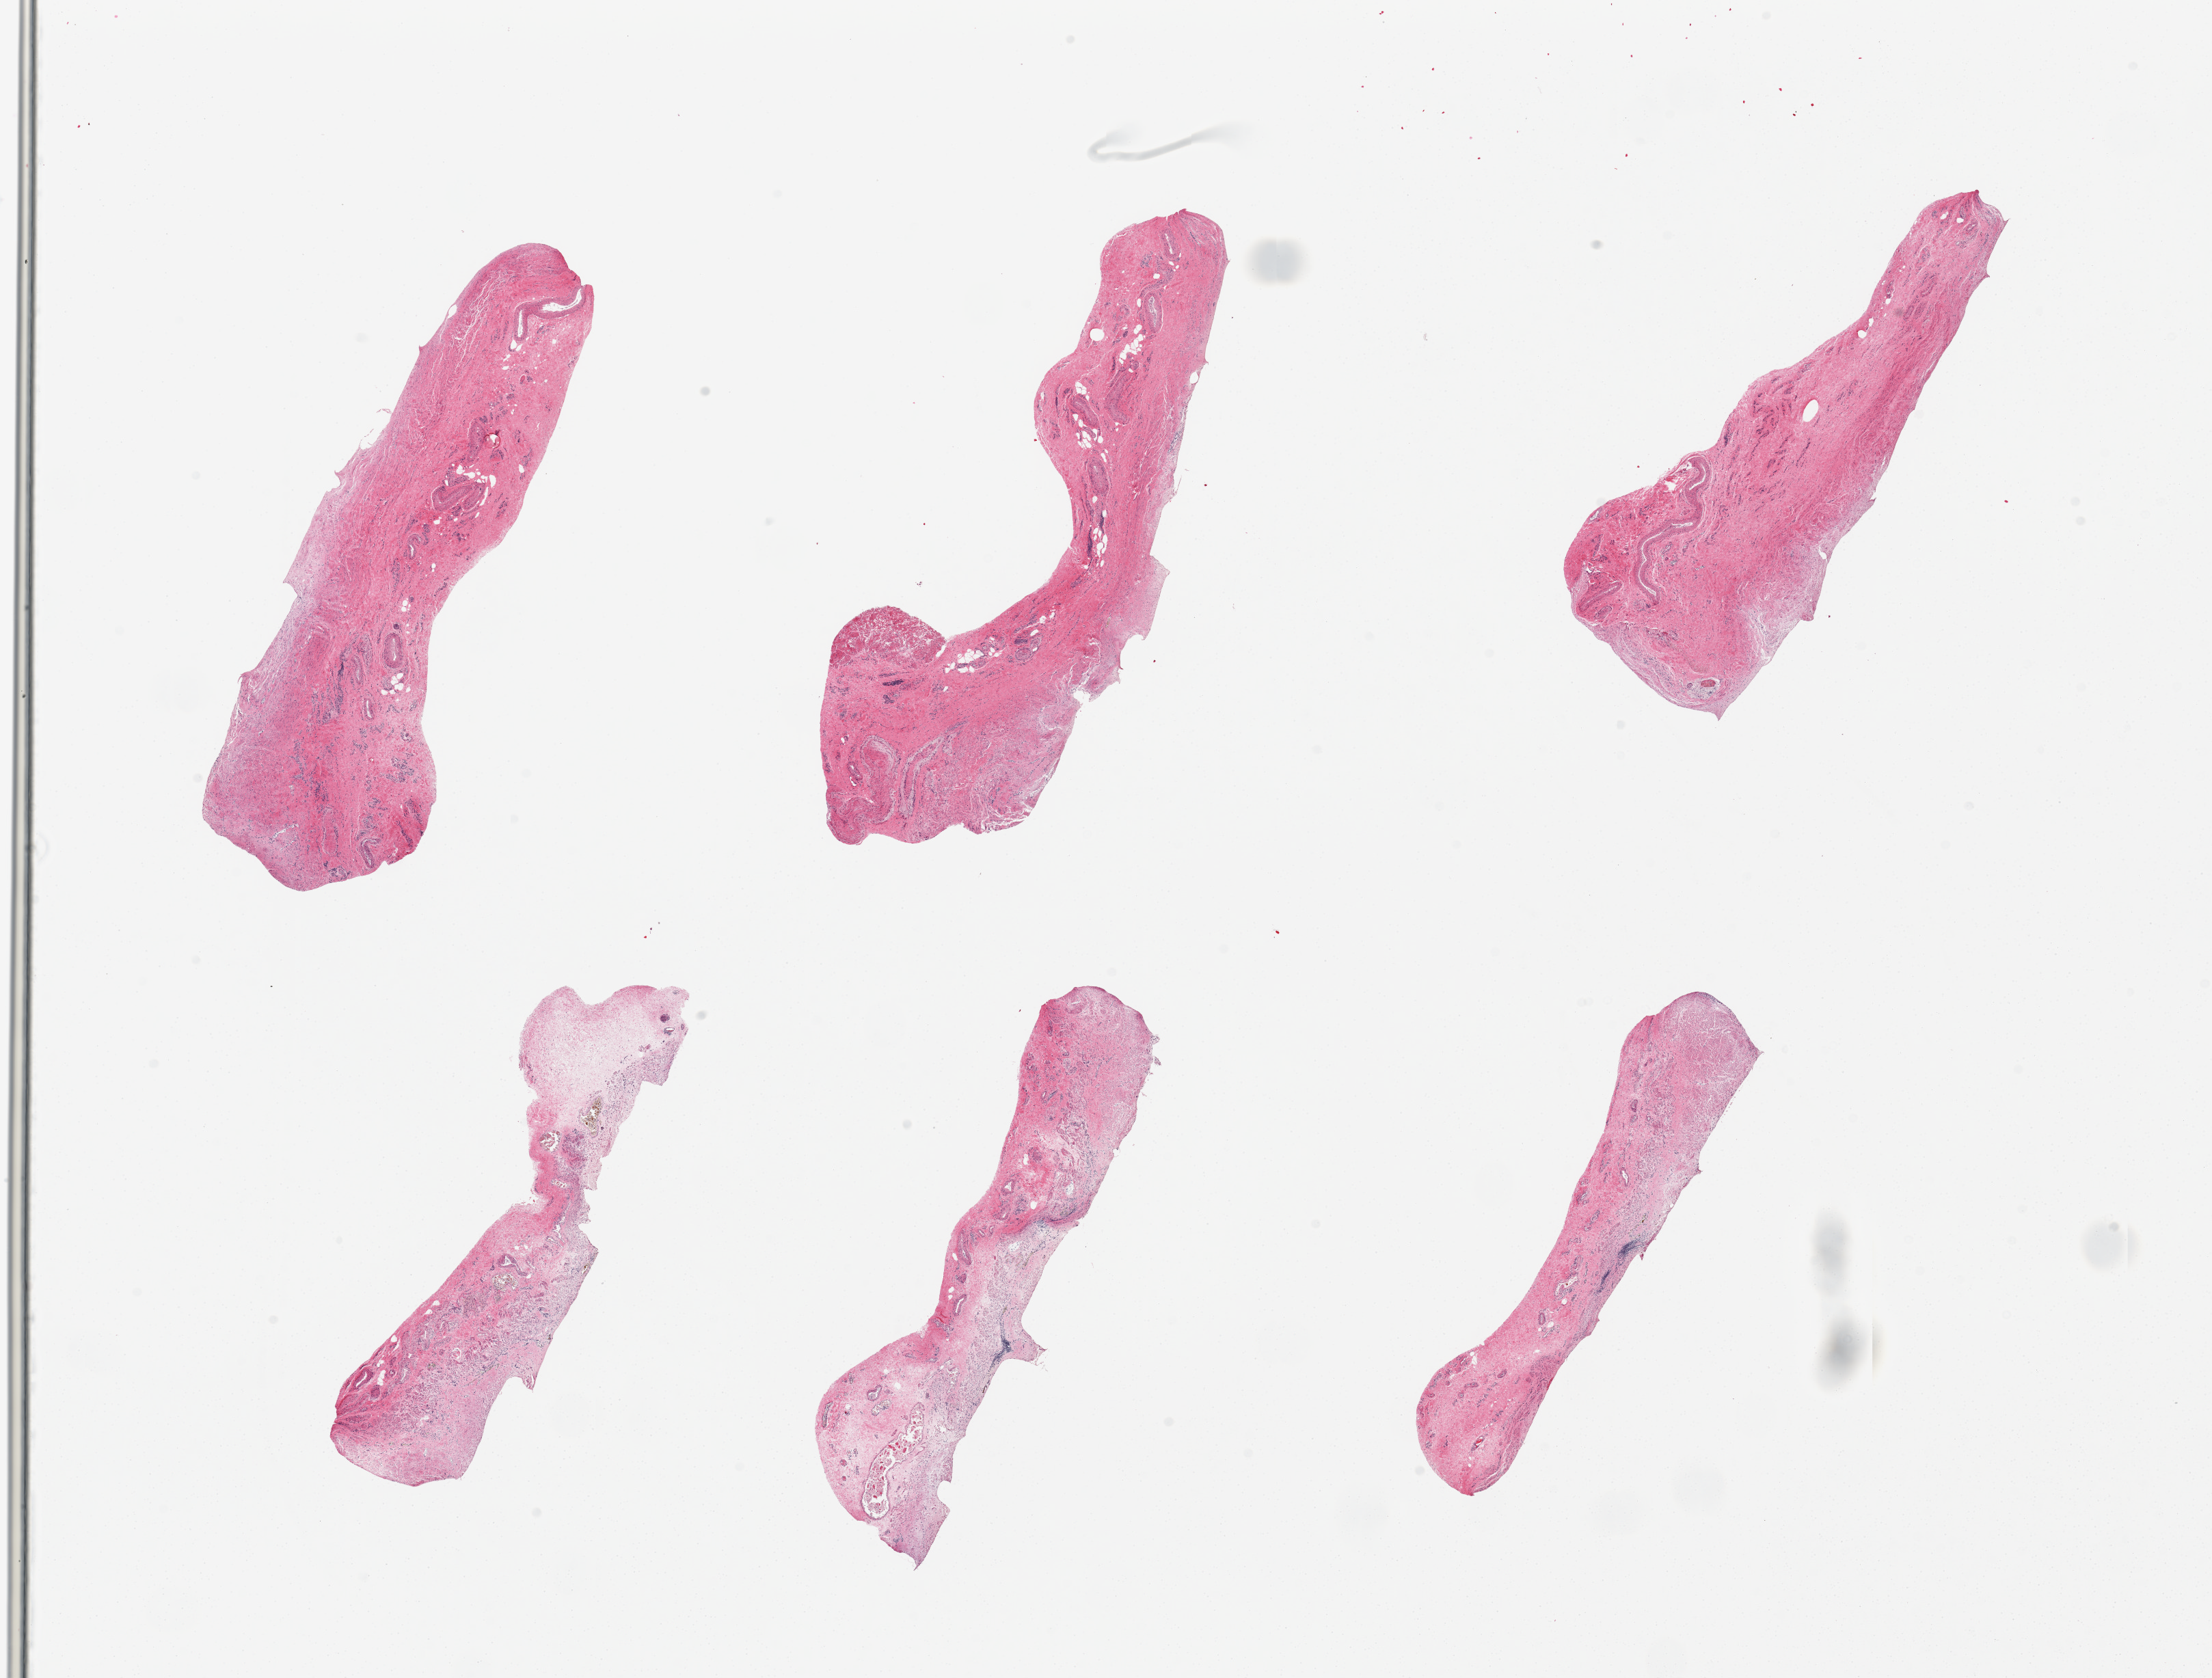
Haematoxylin and eosin whole-slide image, whole scanned area (about 25.6 x 19.4 mm) shown as a low-resolution overview; PAXgene-fixed, paraffin-embedded tissue; section of esophageal mucous membrane (target tissue); tissue donor sample. Donor sex: male.
Reviewer comment on this tissue sample: 6 pieces, fibroadipose/vascular/smooth muscle, no mucosa present. Uknown provenance.